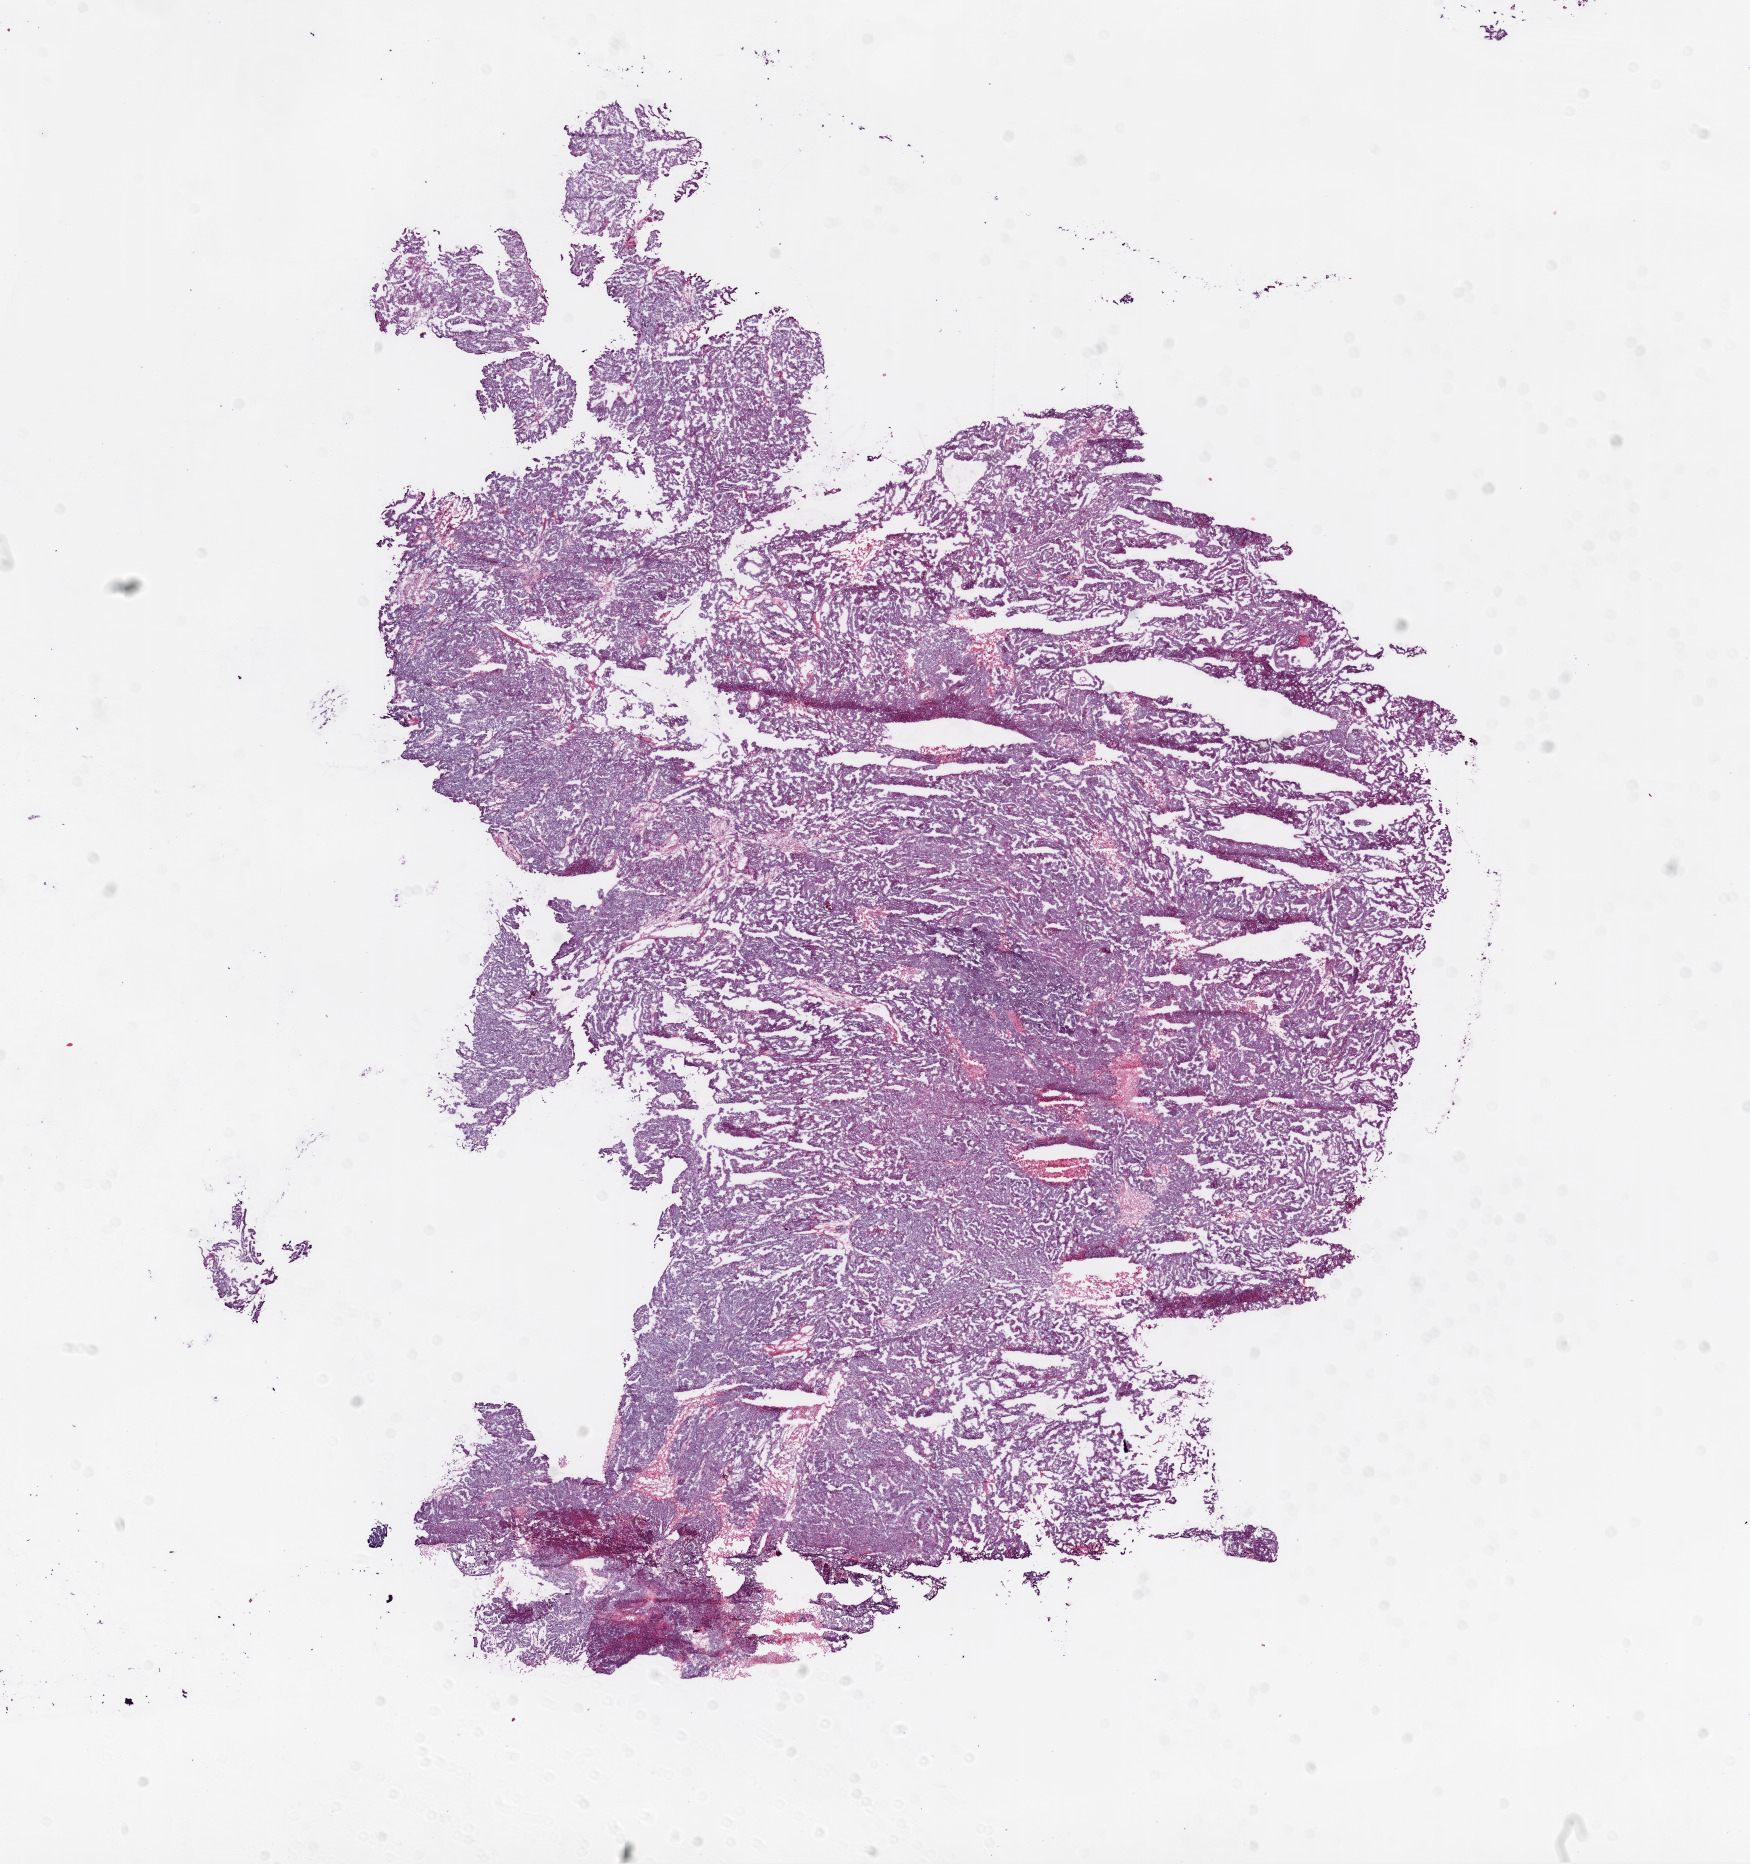
H&E whole-slide image — whole scanned area (about 14.0 x 15.0 mm, slide scanned at 20x) shown as a low-resolution overview, frozen section, ovary, primary tumour sample. Female patient; age at initial diagnosis 58 years. Histologic grade: G3 (poorly differentiated). Composition of this section per pathologist review: tumour cells 98%, tumour nuclei 99%, normal cells 0%, stromal cells 1%, necrosis 1%.
Pathologic diagnosis: Serous cystadenocarcinoma, NOS. Laterality: bilateral. FIGO stage: IIIC.